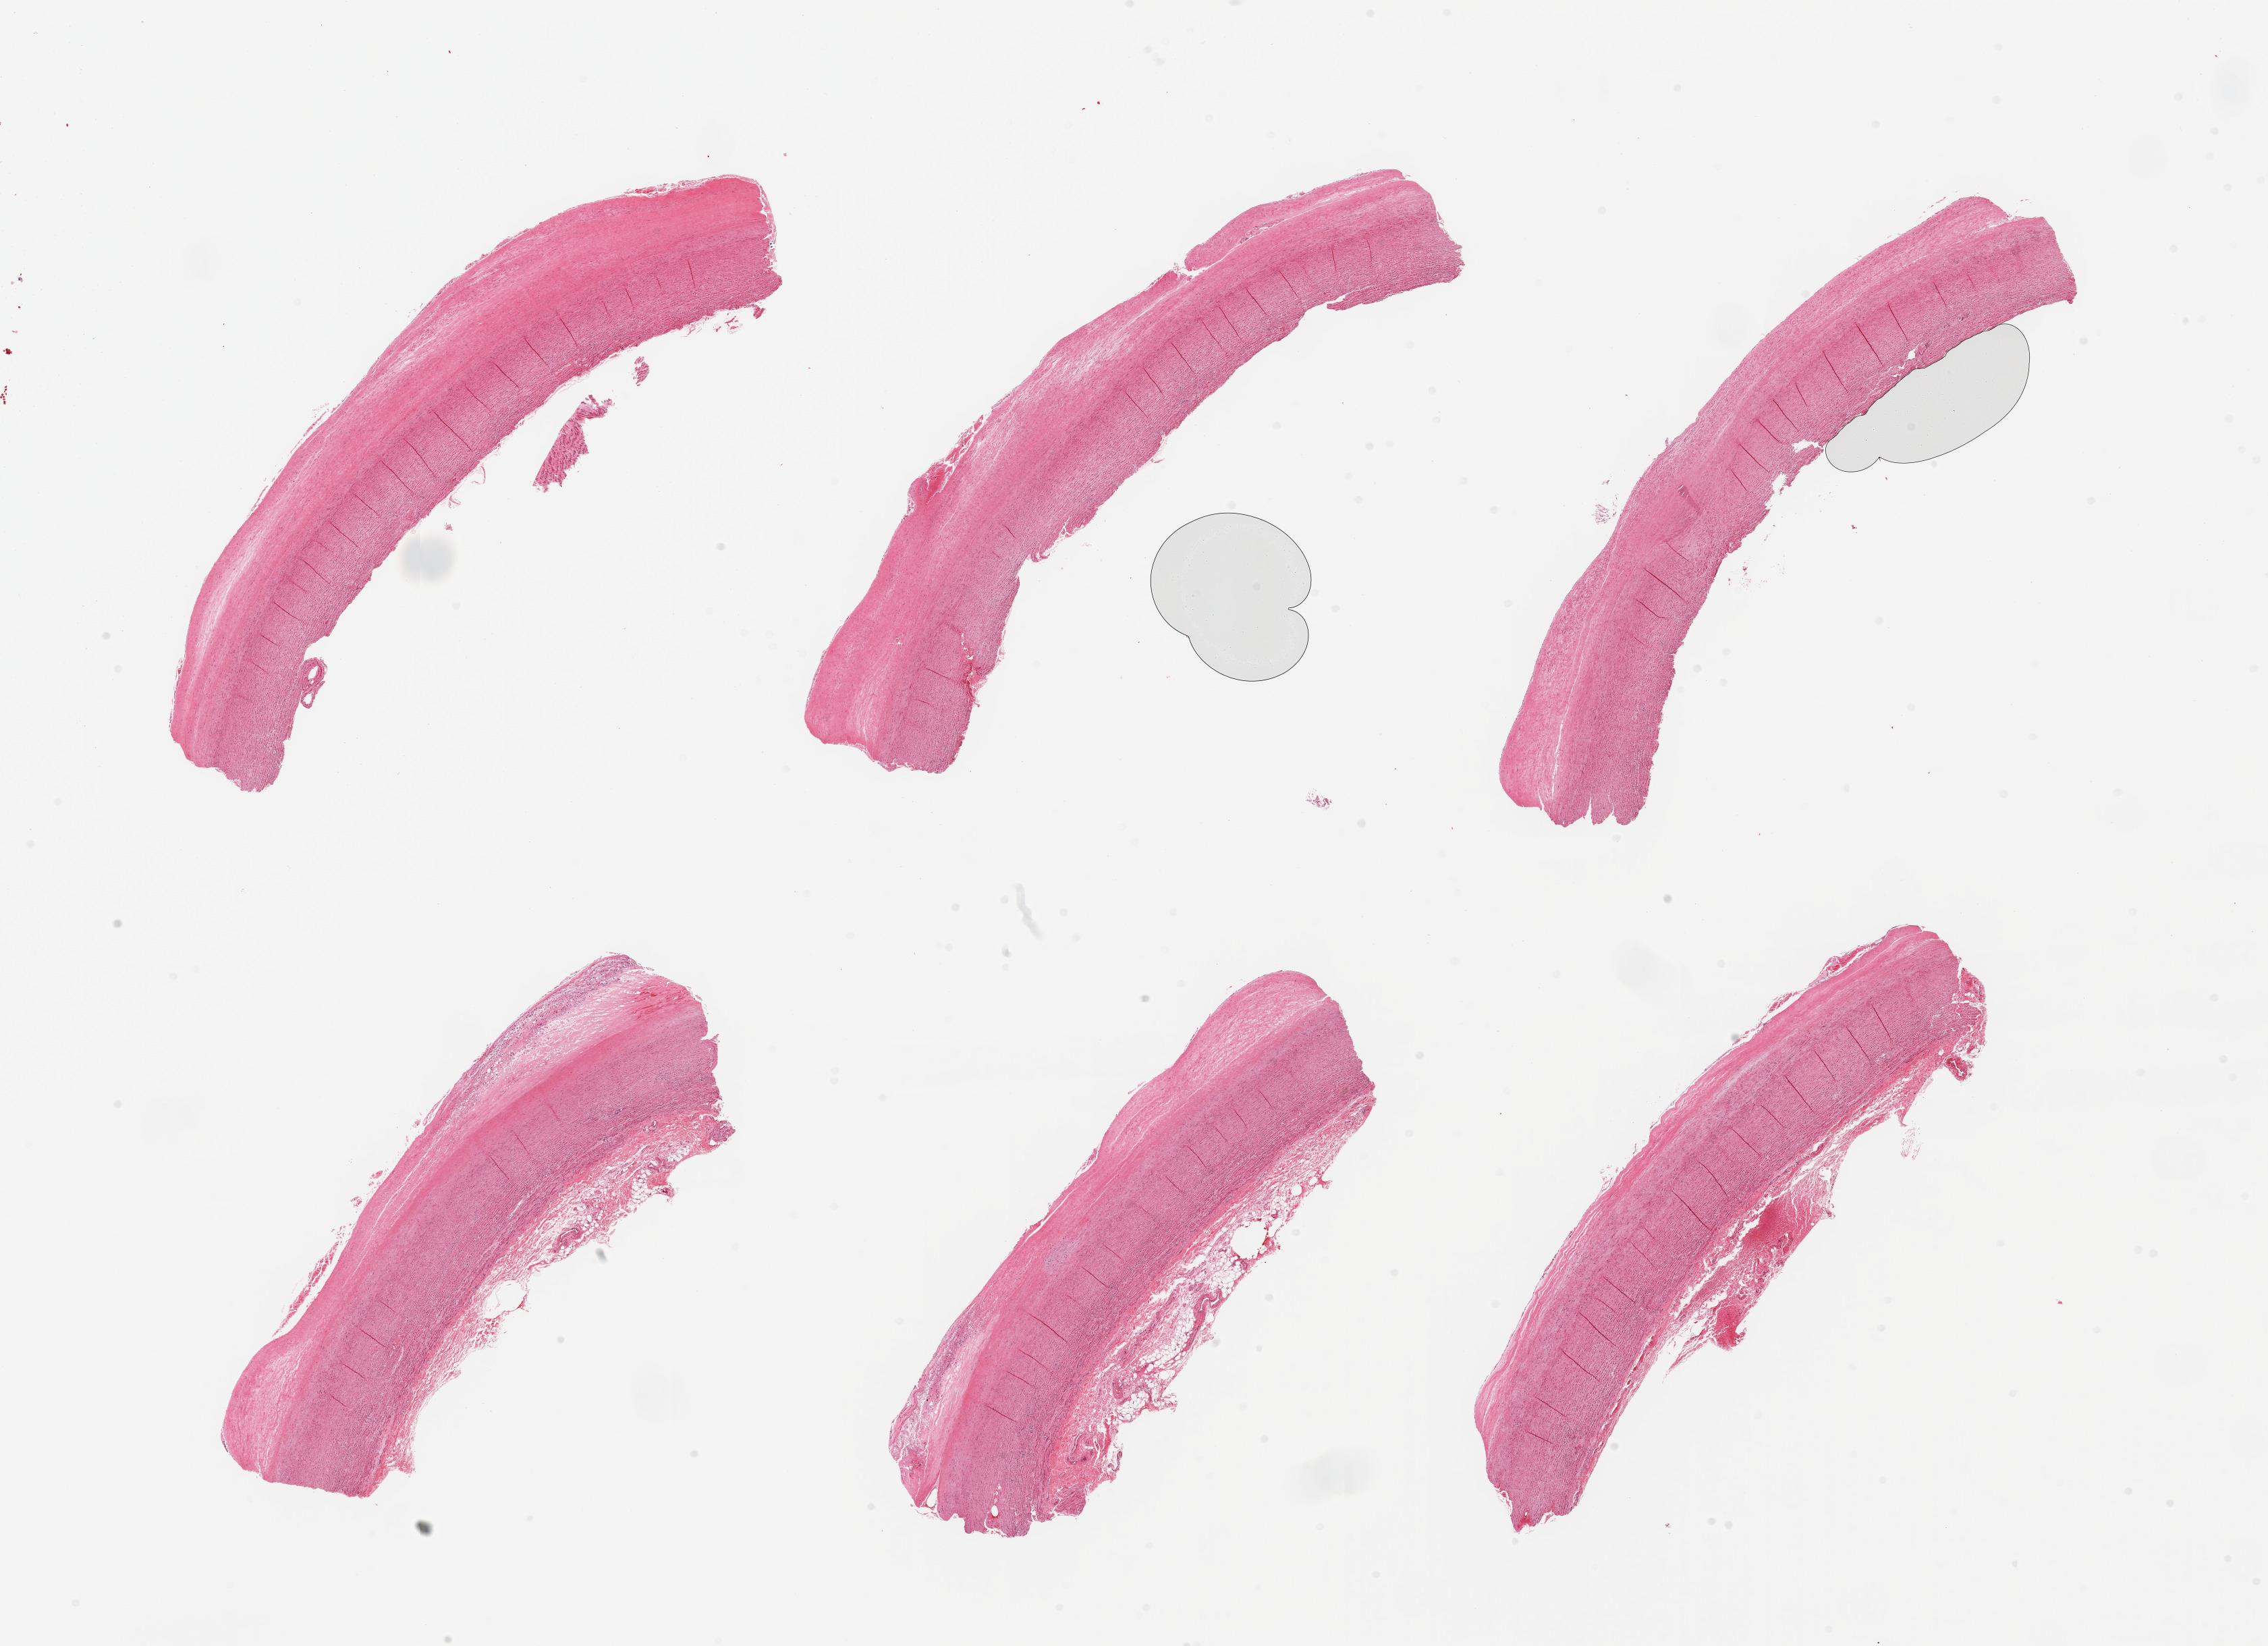
Whole-slide image, haematoxylin and eosin stain — shown as a low-resolution overview of the whole scanned area (about 26.6 x 19.3 mm, from a 20x scan); PAXgene-fixed, paraffin-embedded tissue; sampled site (target tissue): aorta; donor tissue sample. Donor: male.
Reviewer comment on this tissue sample: 6 pieces, atherosis up to ~0.7mm.